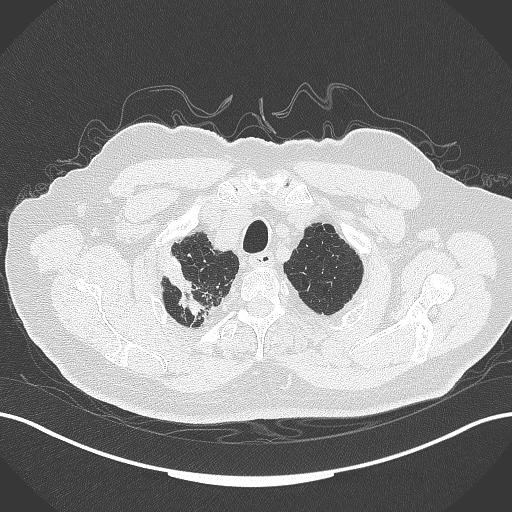
Chest CT, one axial slice; position 322 of 389 along the scan axis; reconstruction kernel B70f; 120 kVp; lung window (W 1500 / L -600 HU); 1 mm slice thickness; 512 × 512 image matrix. Male patient, age 72 years. From the clinical record (not read from this slice): clinical TNM (as recorded): T1a N0 M0.
Annotated regions visible in this slice (rectangle marked by the reading radiologist):
- lung tumour (recorded histology: squamous cell carcinoma): bounding box (x1, y1, x2, y2) in pixels: (165, 253, 204, 314)